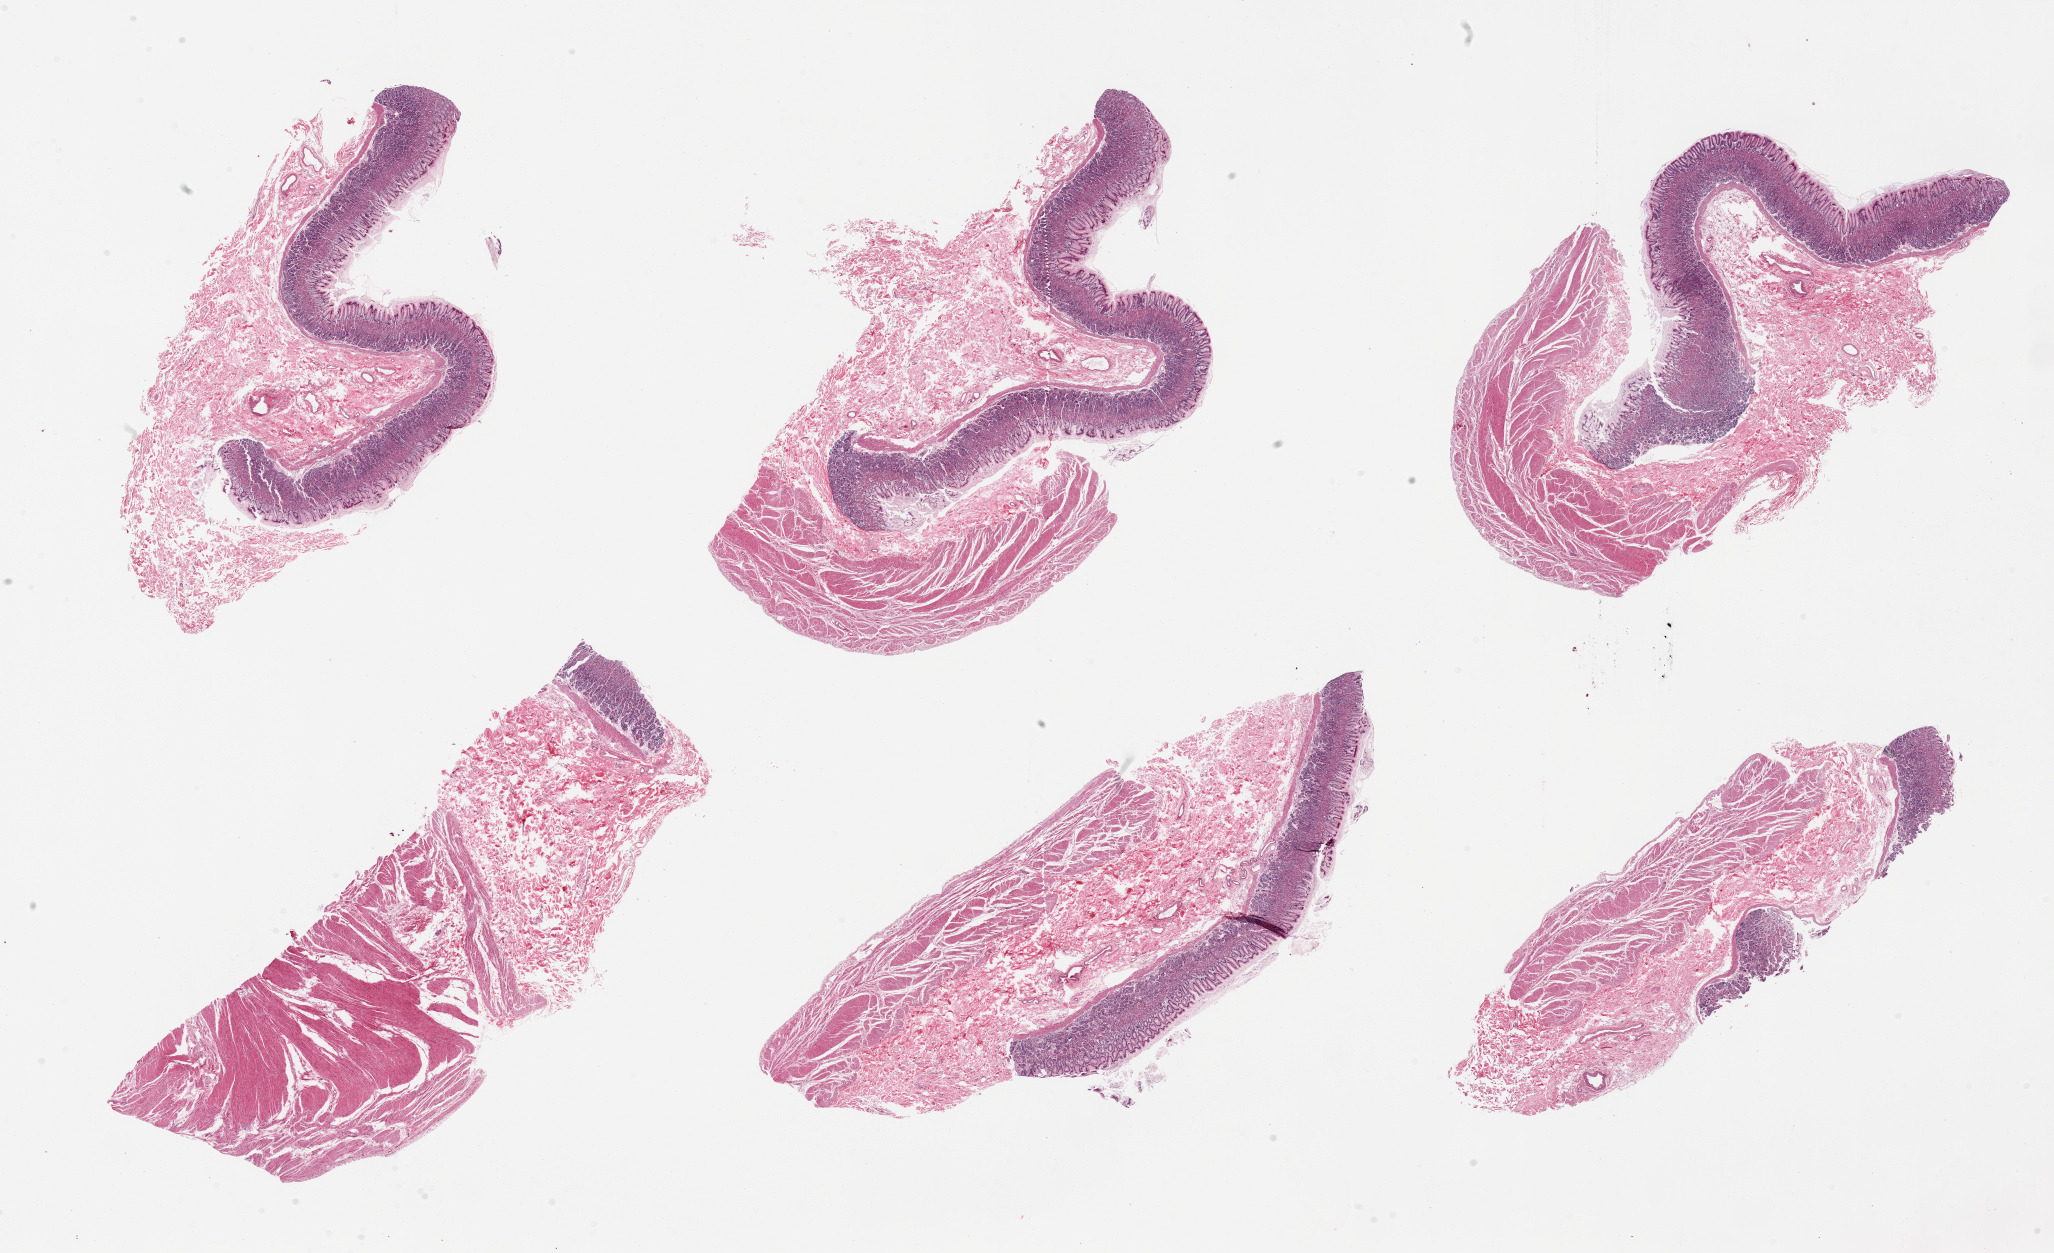
Digitized hematoxylin and eosin (H&E)-stained section — whole scanned area (about 32.5 x 19.8 mm) shown as a low-resolution overview, PAXgene-fixed, paraffin-embedded tissue, sampled site (target tissue): stomach, donor tissue sample. Male donor.
Reviewer comment on this tissue sample: 6 pieces; well preserved mucosa and muscularis.